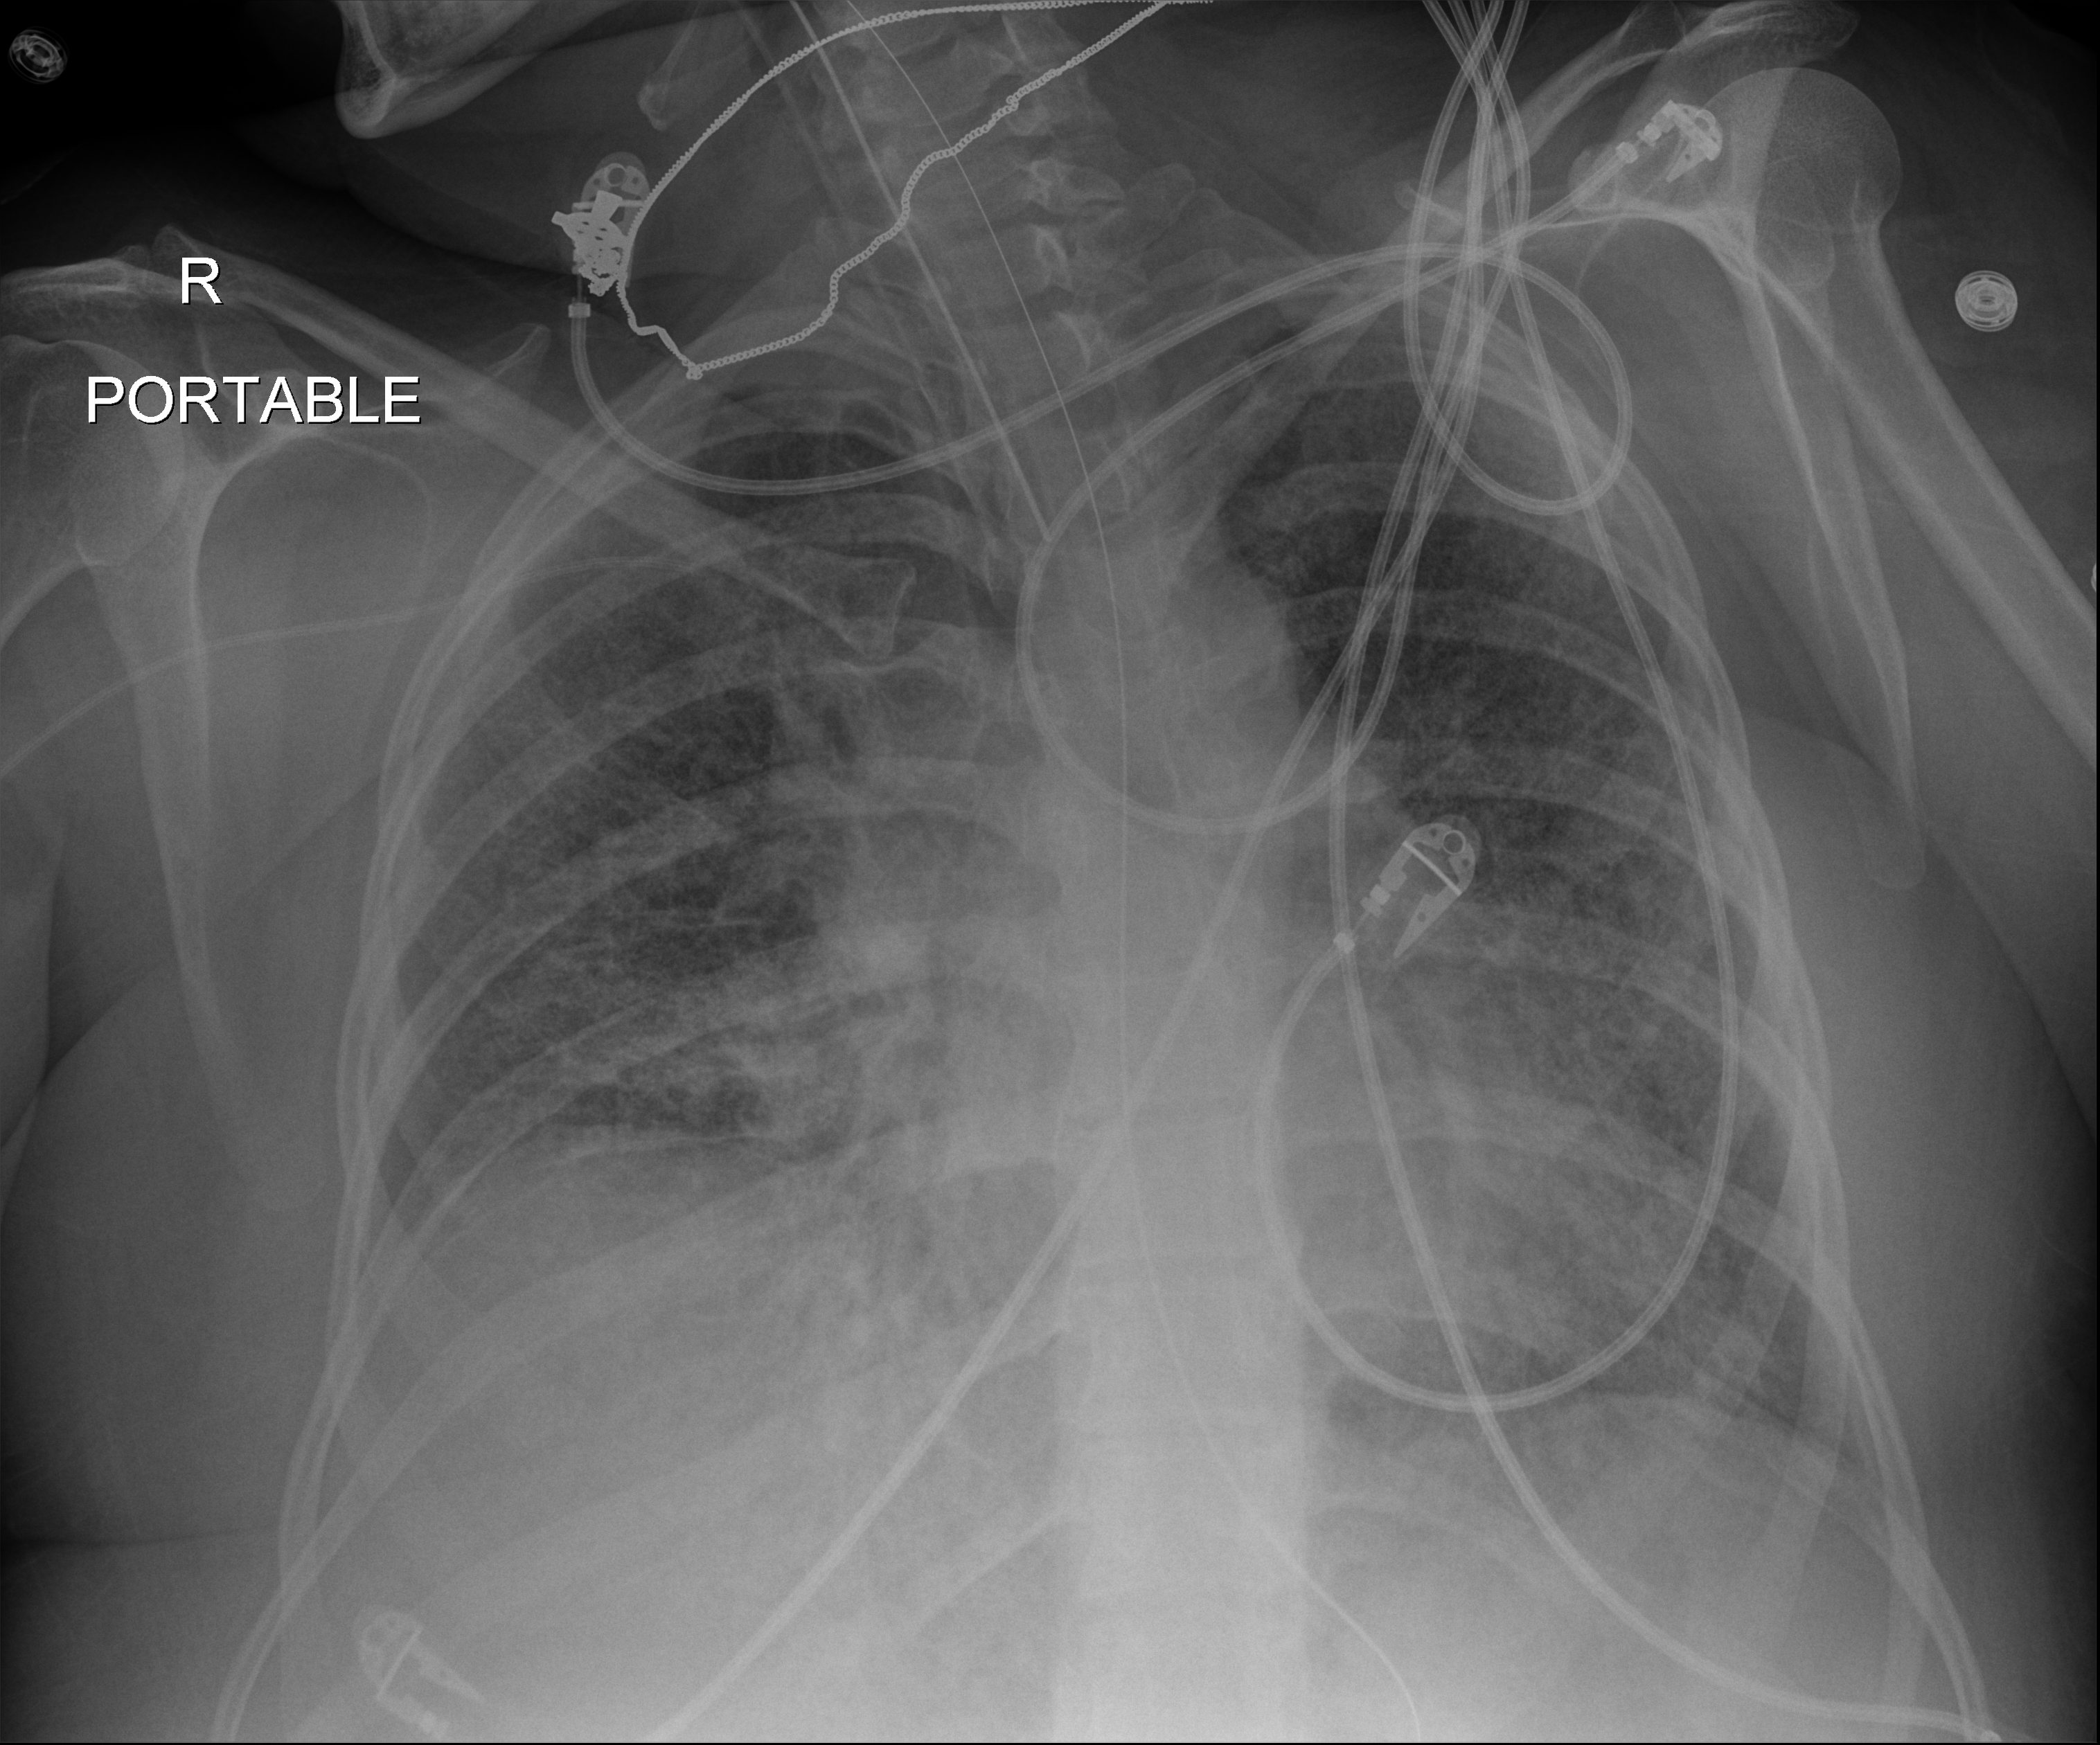
Chest X-ray; anteroposterior (AP) projection. Patient hospitalised with COVID-19; female, aged 18–59 years.
Hospital-stay facts (about this admission, not read from this image; timing relative to this image not recorded): admitted to intensive care during this hospital stay: yes; mechanically ventilated during this hospital stay: yes; diabetes (admission record): no.